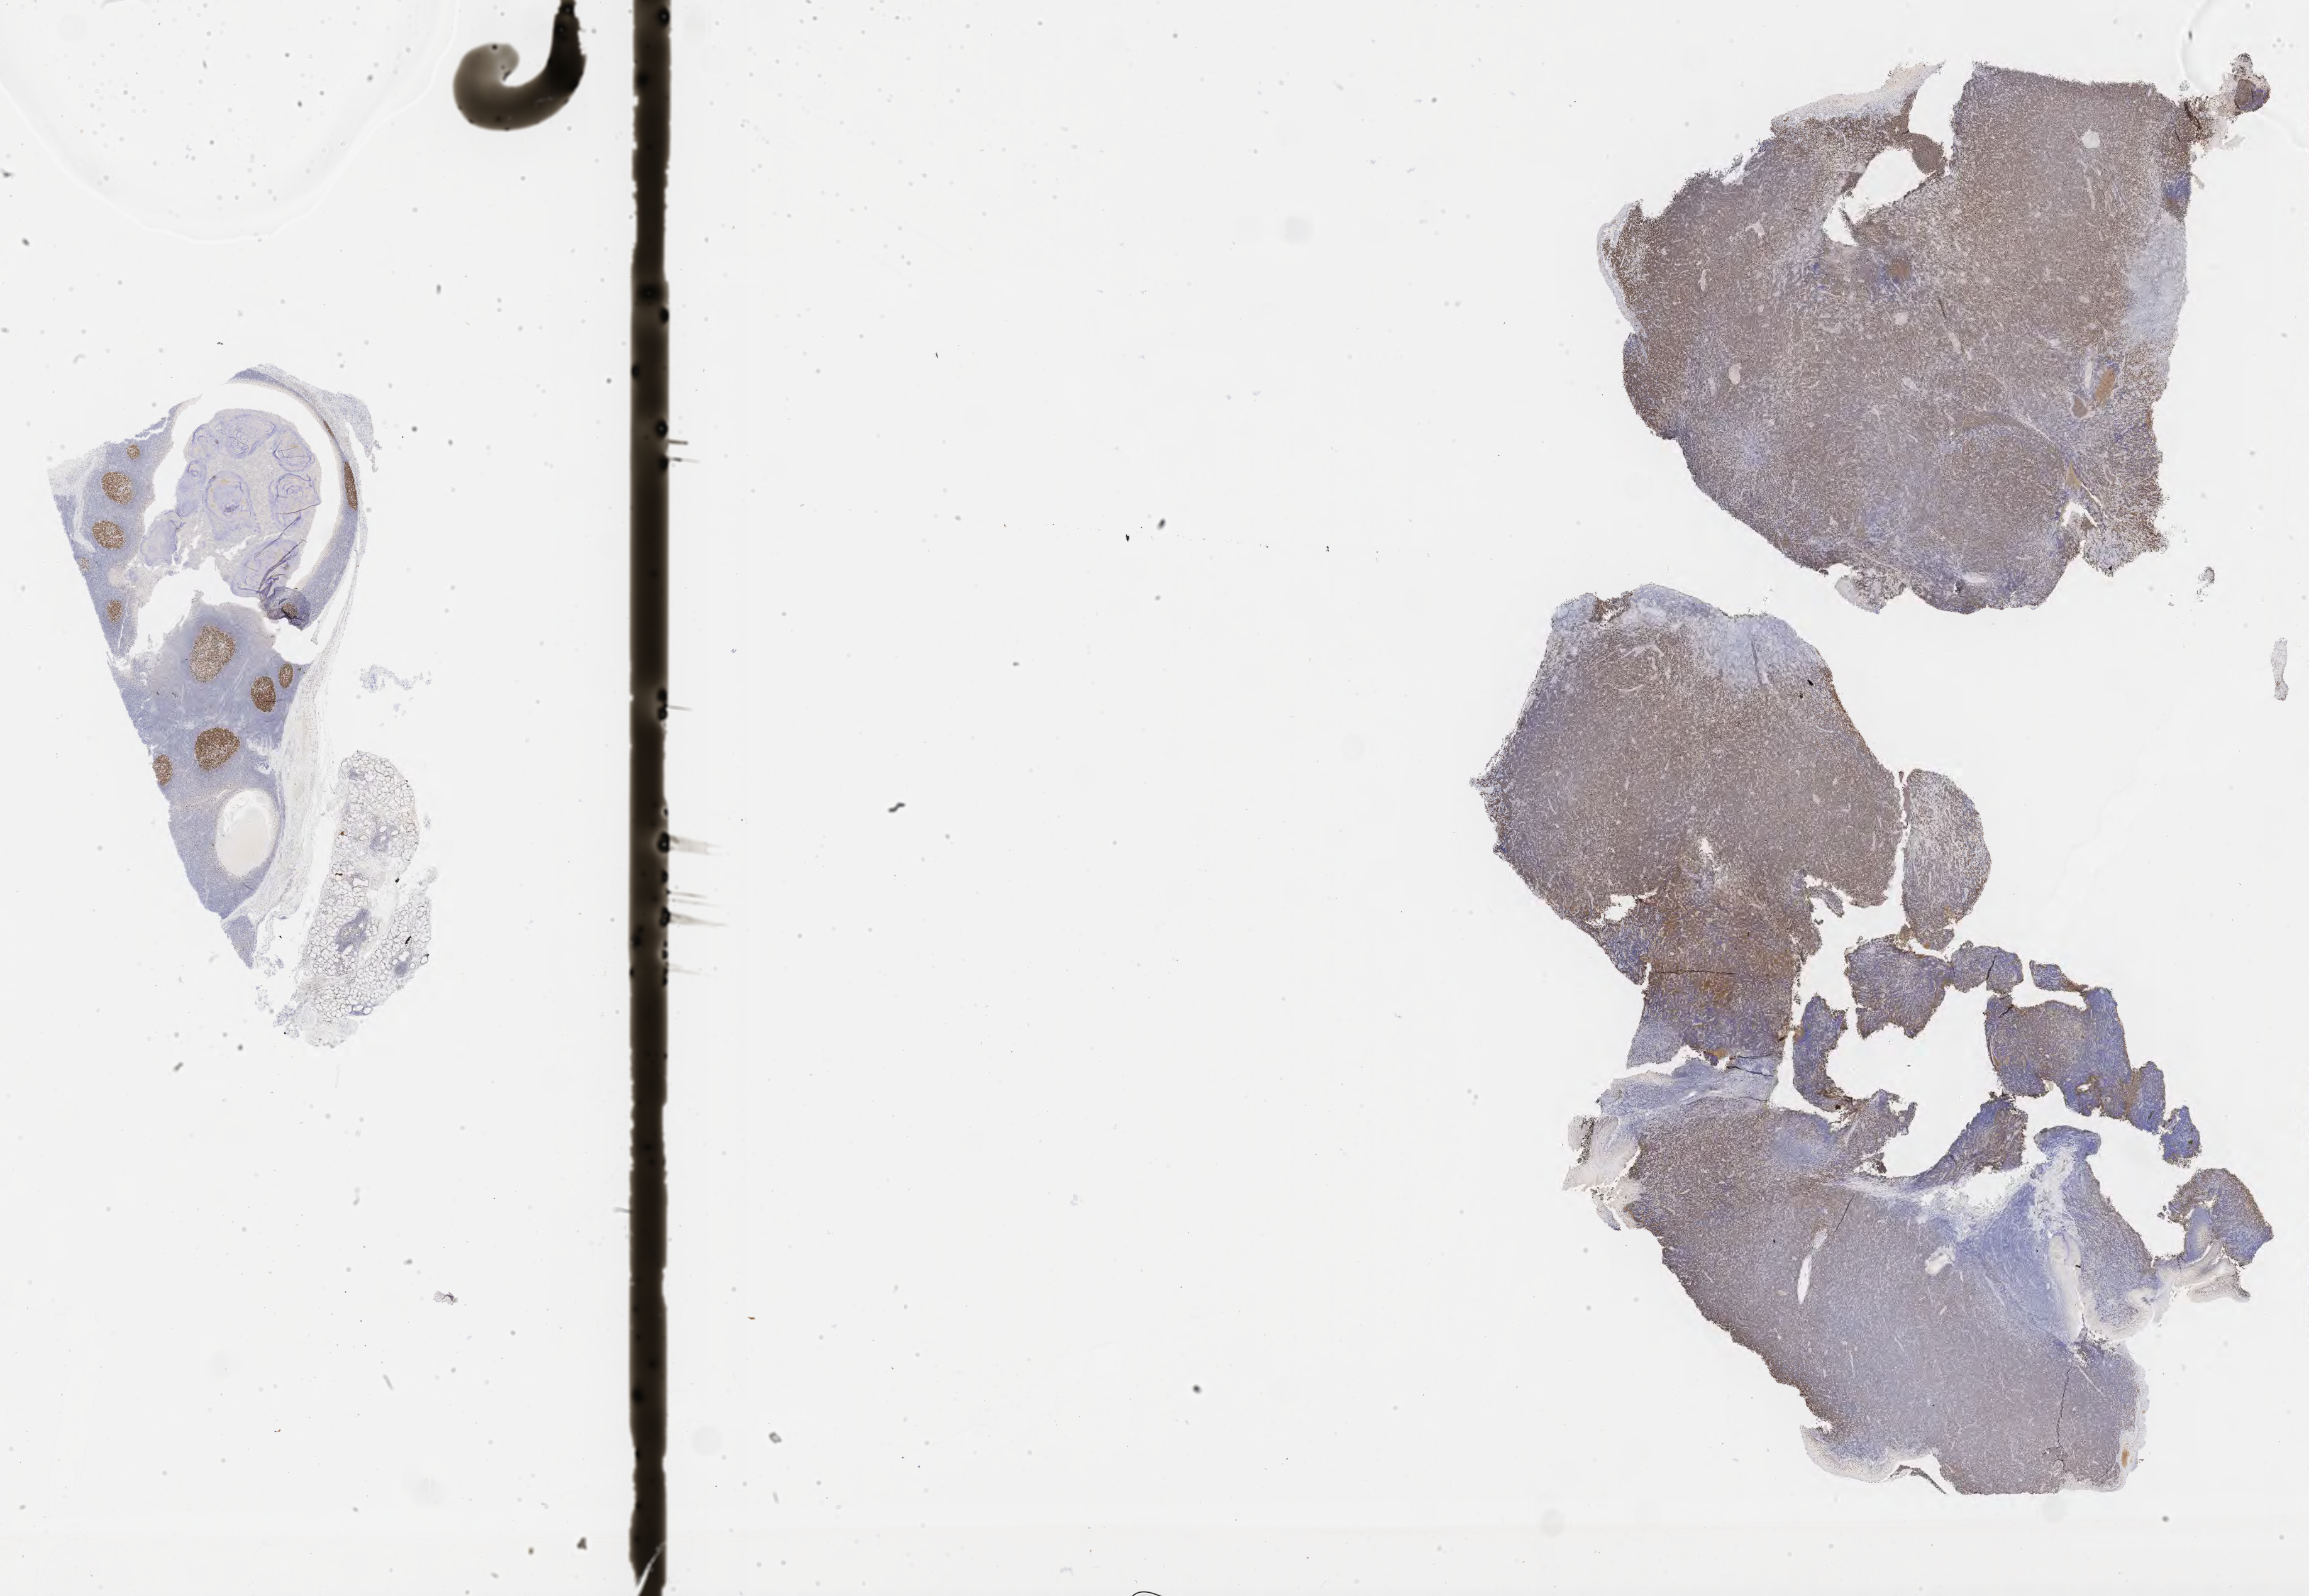
IHC for BCL6, whole-slide image — a low-resolution overview of the entire scanned area, about 29.7 x 20.5 mm, specimen: tumor tissue. Patient male; 22 years old.
Histologic diagnosis: Diffuse large B-cell lymphoma, NOS.